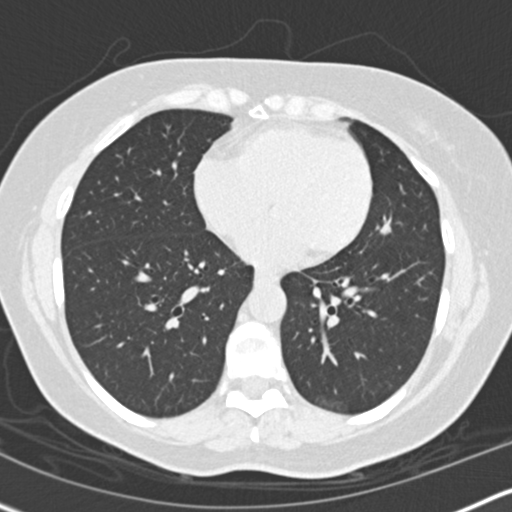
Axial slice from a low-dose chest CT screening exam; second annual screen; lung window (W 1500 / L -600 HU); 2 mm slice thickness; standard (soft-tissue) reconstruction kernel (B30f); 120 kVp. Female participant, aged 56 years at enrolment. Former smoker at enrolment.
Lesion marked by an expert reader, bounding box (x1, y1, x2, y2) in pixels: (357, 203, 408, 254). Screening reader's record for this exam (one nodule recorded; not confirmed to be the boxed lesion): non-calcified nodule or mass ≥4 mm, lingula, 10 × 8 mm, smooth margins, soft tissue attenuation, pre-existing on the prior screen: yes; interval growth: yes. Official screen result: positive, other. Later outcome: lung cancer diagnosed 506 days after this screen (after the third annual screen) — adenocarcinoma, NOS, left upper lobe, poorly differentiated (G3), stage IIIA (AJCC 6th edition), 15 mm at pathology.